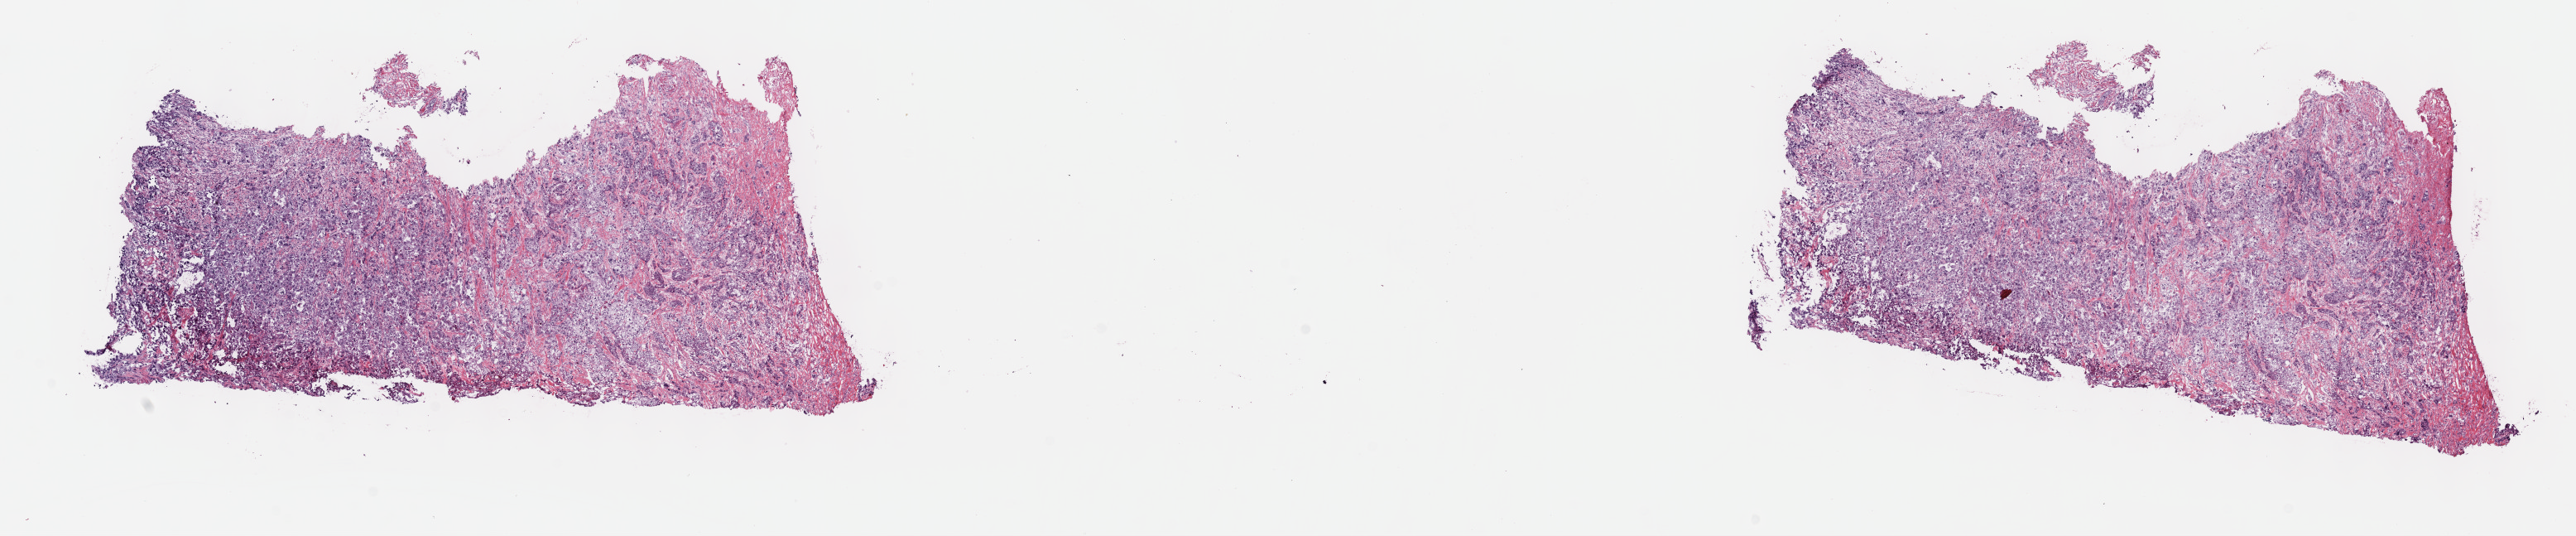
Digitized Hematoxylin and eosin (H&E) stained tissue section (whole slide) — shown as a low-resolution overview of the whole scanned area (about 25.2 x 5.2 mm); frozen section from the top of the tissue portion; sample: primary tumour, lung. Male patient; age at initial diagnosis 71 years. Pathologist review of this section (percent, as recorded): tumour cells 70%, tumour nuclei 70%.
Pathologic diagnosis: Squamous cell carcinoma, NOS.